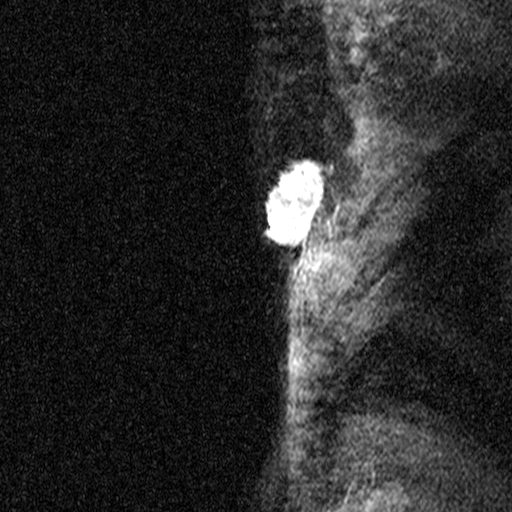
Breast MRI (dynamic contrast-enhanced), one sagittal slice; position 37 of 44 along the scan axis; dynamic contrast-enhanced study with each time point stored as its own series, time point 2 of 3 at this slice position (early post-contrast, ordered by acquisition time); 1.5 T; TE 4.5 ms, TR 11 ms; 512 × 512 image matrix. Patient: female, 44 years. Case-level facts recorded for this patient, not image findings: setting: breast cancer imaged before/during neoadjuvant chemotherapy; receptor status: HR-positive, HER2-negative.
Outlined on this slice (semi-automatic segmentation, software-assisted and operator-edited):
- analysis volume of interest (the breast-tissue region the enhancement analysis was run in; not a lesion): box from (x=218, y=118) to (x=341, y=291) px
- tumour enhancement mask (voxels above the 90 % enhancement threshold inside the analysis volume of interest): (x=266, y=160)–(x=333, y=248)